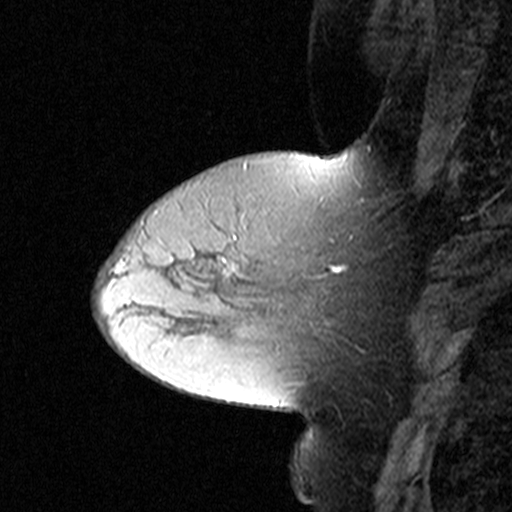
Breast MRI (dynamic contrast-enhanced), one sagittal slice; slice 14 of 44 in the series (ordered by position); dynamic contrast-enhanced study with each time point stored as its own series, time point 2 of 3 at this slice position (early post-contrast, ordered by acquisition time); 1.5 T; TE 4.5 ms, TR 11 ms; 3 mm slice thickness; 512 × 512 image matrix, field of view 200 × 200 mm. Female patient, age 50 years. From the clinical record (not read from this slice): setting: breast cancer imaged before/during neoadjuvant chemotherapy; receptor status: HR-positive, HER2-negative.
Structures marked on this image (semi-automatically segmented with operator editing):
- analysis volume of interest (the breast-tissue region the enhancement analysis was run in; not a lesion): box from (x=180, y=198) to (x=310, y=311) px
- tumour enhancement mask (voxels above the 90 % enhancement threshold inside the analysis volume of interest): (x=223, y=257)–(x=238, y=269)